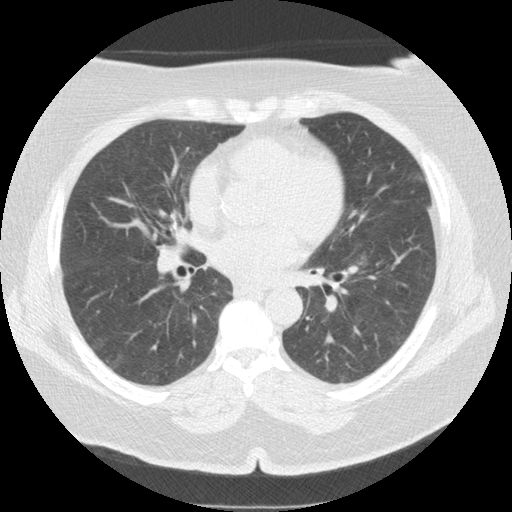
Low-dose screening chest CT, axial slice, first (baseline) screen, lung window (W 1500 / L -600 HU), standard (soft-tissue) reconstruction kernel (STANDARD), 120 kVp. Female participant, aged 65 years at enrolment.
Expert-annotated lung lesion, box from (x=346, y=242) to (x=379, y=279) px. Screening reader's record for this exam: no non-calcified nodule ≥4 mm recorded. Official screen result: negative screen, minor abnormalities not suspicious for lung cancer. Later outcome: lung cancer diagnosed 986 days after this screen — adenocarcinoma, NOS, left lower lobe, moderately differentiated (G2), stage IA (AJCC 6th edition), 12 mm at pathology.